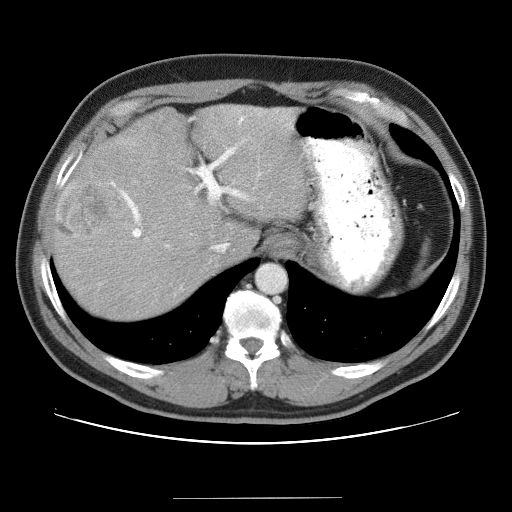
Contrast-enhanced abdominal CT (liver protocol), one axial slice; slice 28 of 40 in the series (ordered by position); soft-tissue window (W 400 / L 40 HU); 5 mm slice thickness; 512 × 512 image matrix. Case-level facts recorded for this patient, not image findings: diagnosis: hepatocellular carcinoma (patient treated with transarterial chemoembolisation; whether this scan precedes or follows treatment is not stated here); TNM stage (as recorded): Stage-IVA; Child-Pugh class: B; tumour nodularity: multinodular.
Annotated regions visible in this slice (semi-automatic segmentation, software-assisted and operator-edited):
- abdominal aorta: box from (x=256, y=265) to (x=285, y=293) px
- liver parenchyma outside the tumour (the mass and vessels are separate outlines, so this box may not span the whole liver): (x=54, y=104)–(x=308, y=318)
- mass: (x=55, y=181)–(x=119, y=241)
- liver vessels: (x=111, y=112)–(x=278, y=247)